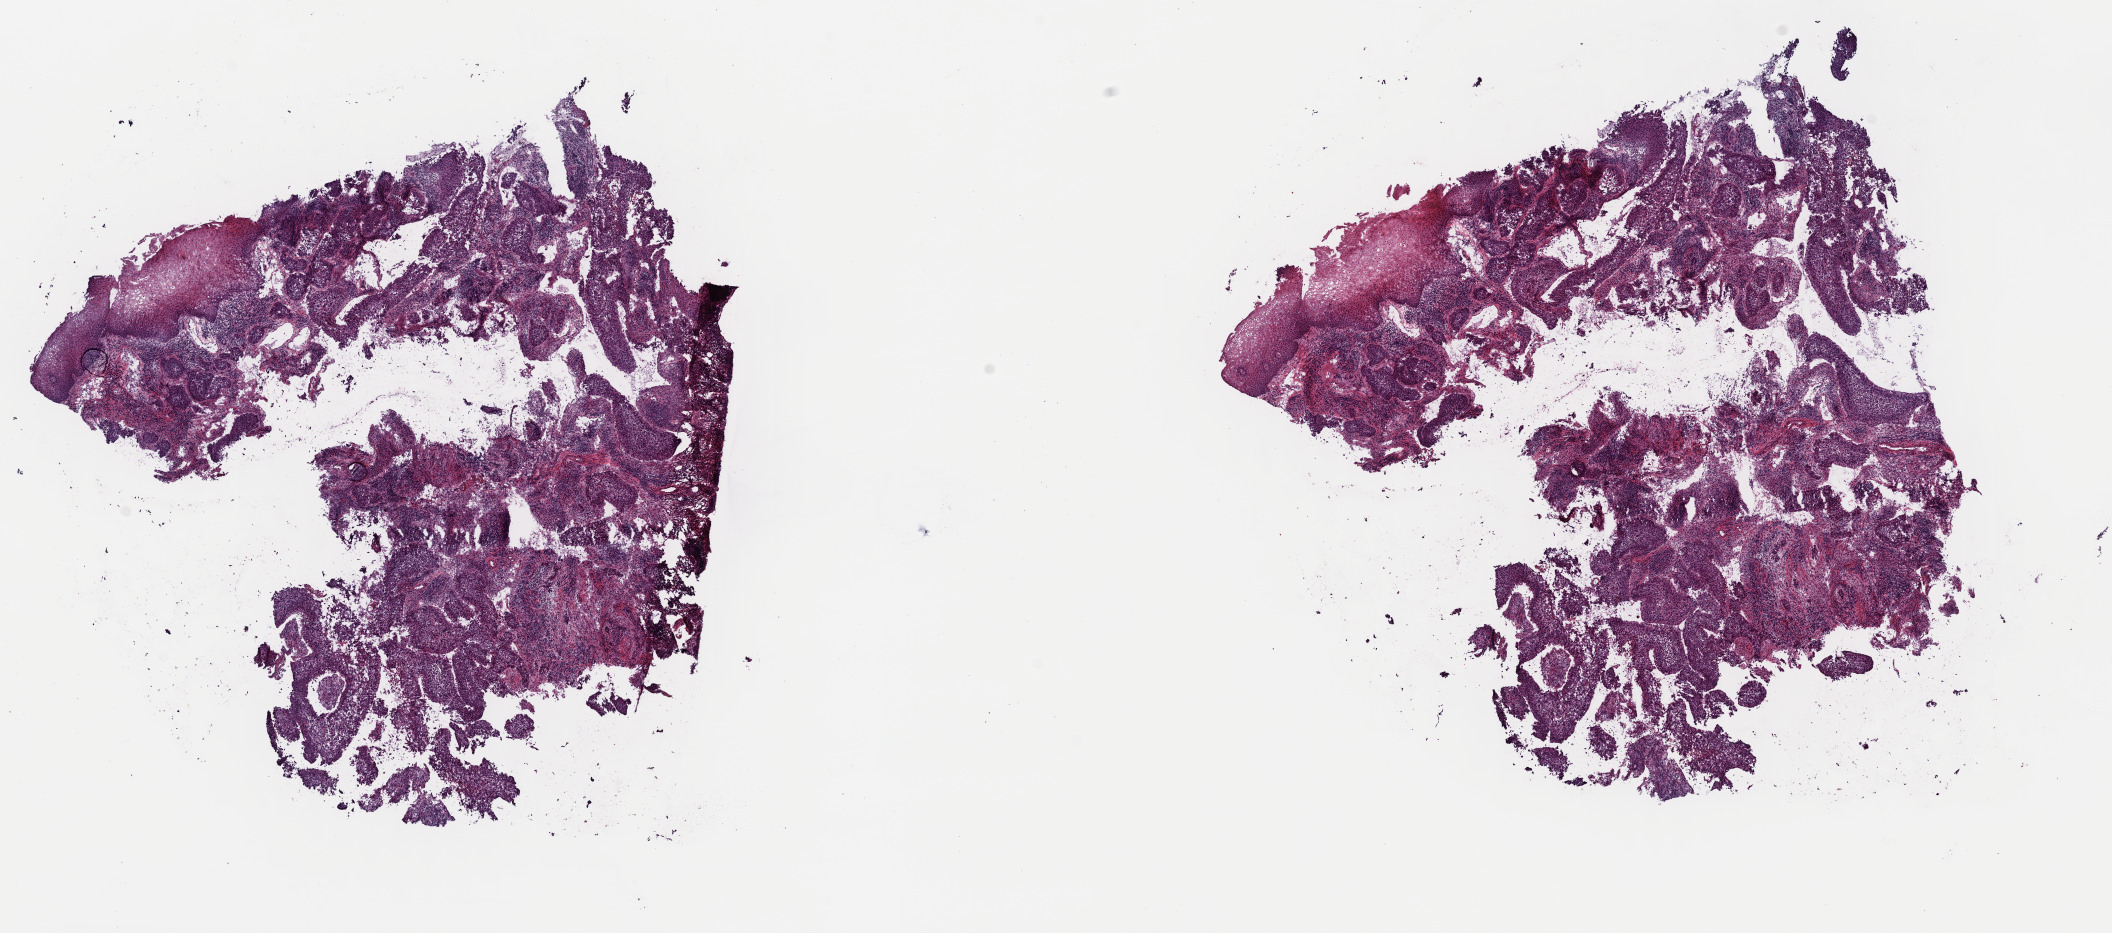
H&E whole-slide image — low-resolution overview of the scanned area, about 16.7 x 7.4 mm (slide scanned at 40x), frozen section from the top of the tissue portion, primary tumour sample from the cervix. Patient: female, age at initial diagnosis 45 years. Histologic grade: G3 (poorly differentiated). Slide review estimates, as recorded: tumour cells 90%, tumour nuclei 90%, normal cells 0%, stromal cells 5%, necrosis 5%. Infiltration values recorded for this section: lymphocyte infiltration 40%, monocyte infiltration 20%, neutrophil infiltration 20%.
FIGO stage: IIB. Histologic diagnosis: Squamous cell carcinoma, large cell, nonkeratinizing, NOS (cervix uteri).